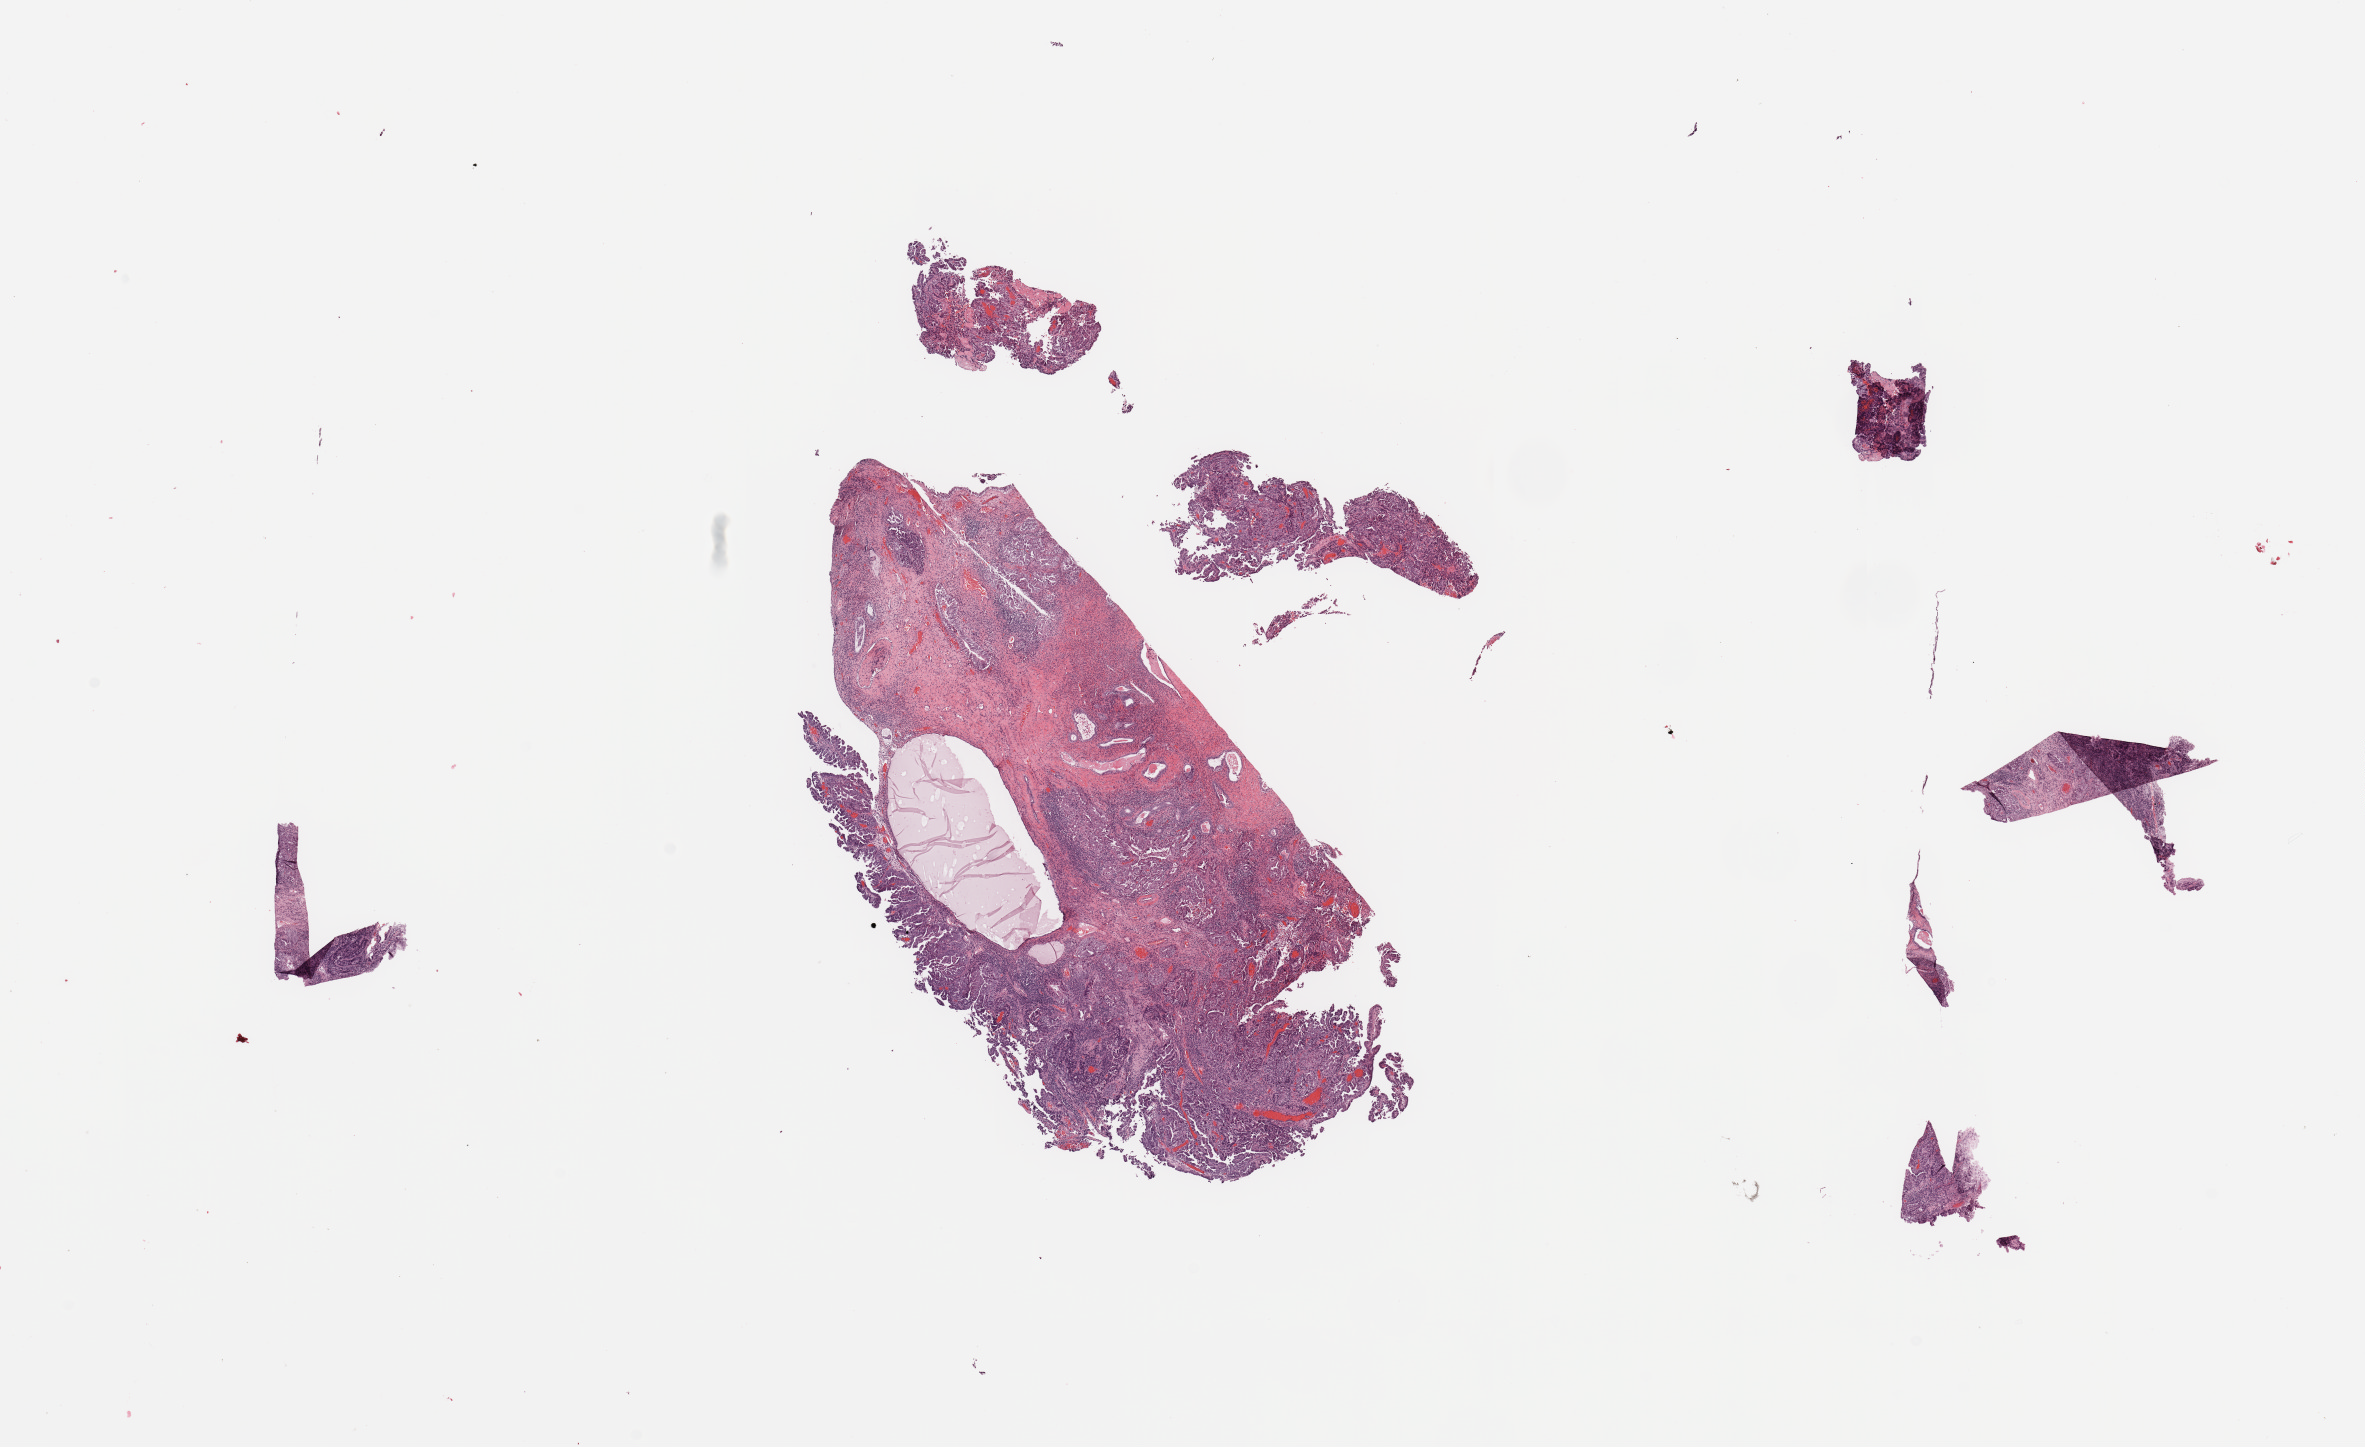
H&E whole-slide image, low-resolution overview of the scanned area, about 18.7 x 11.4 mm. Tumour tissue sample, sampled site: uterus. Patient: female, age 81 years. Histologic grade: G3 (poorly differentiated). Composition of this section per pathologist review: tumour nuclei 80%, necrosis 0%.
Diagnosis: Endometrioid adenocarcinoma, NOS. AJCC pathologic stage: II.